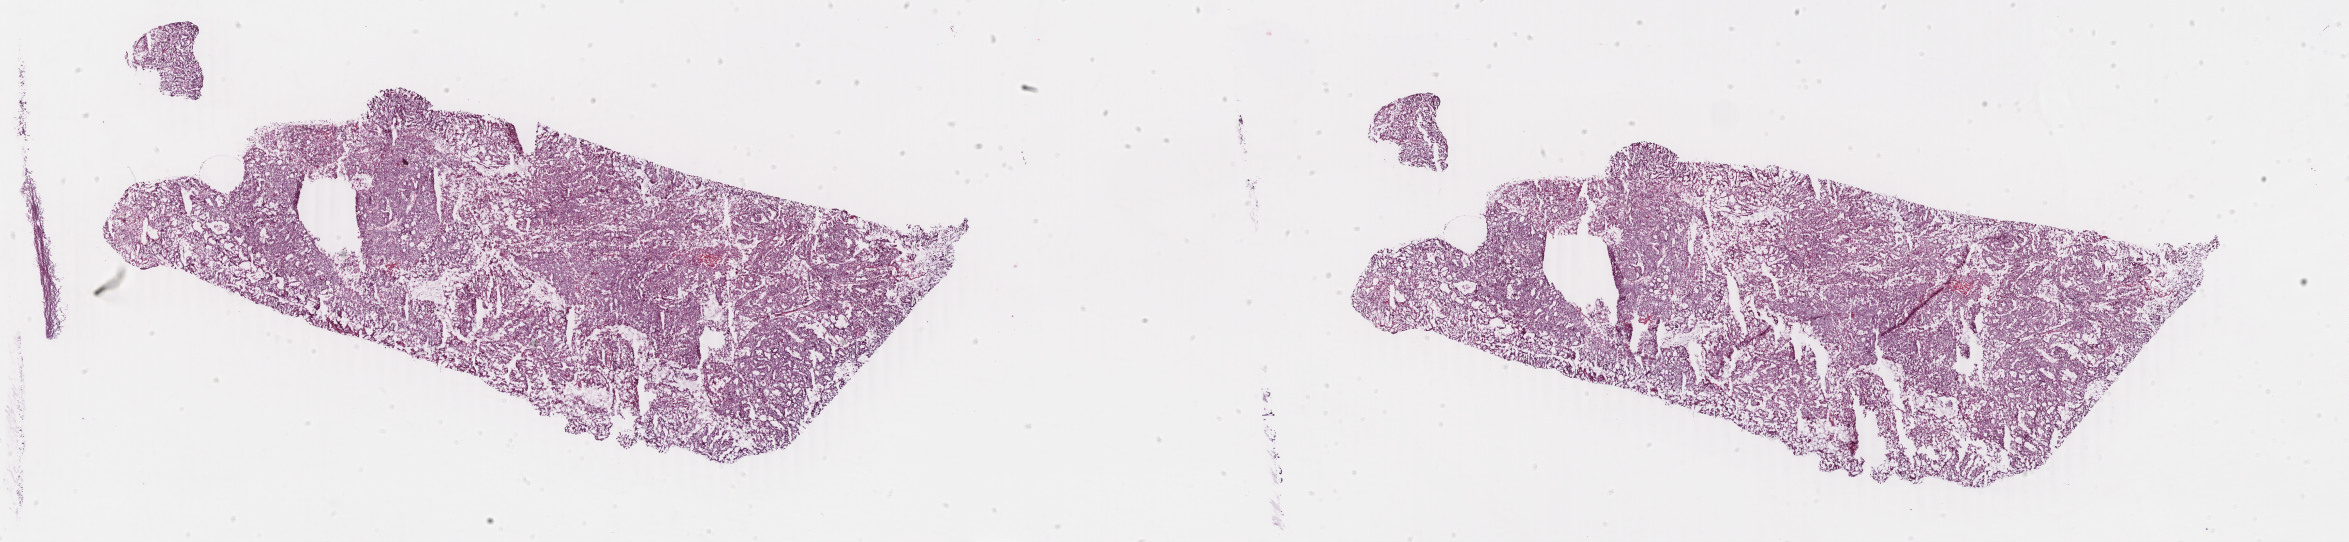
Digitized H&E-stained tissue section (whole slide), whole scanned area (about 37.4 x 8.6 mm) shown as a low-resolution overview. Frozen section from the top of the tissue portion. Sample: primary tumour, uterus. Female, age 60 years at initial diagnosis. Histologic grade: G1 (well differentiated). Composition of this section per pathologist review: tumour cells 85%, tumour nuclei 95%, normal cells 3%, stromal cells 2%, necrosis 10%. Inflammatory infiltration, as recorded: lymphocyte infiltration 3%, monocyte infiltration 0%, neutrophil infiltration 0%.
• diagnosis: Endometrioid adenocarcinoma, NOS (endometrium)
• FIGO stage: IIB